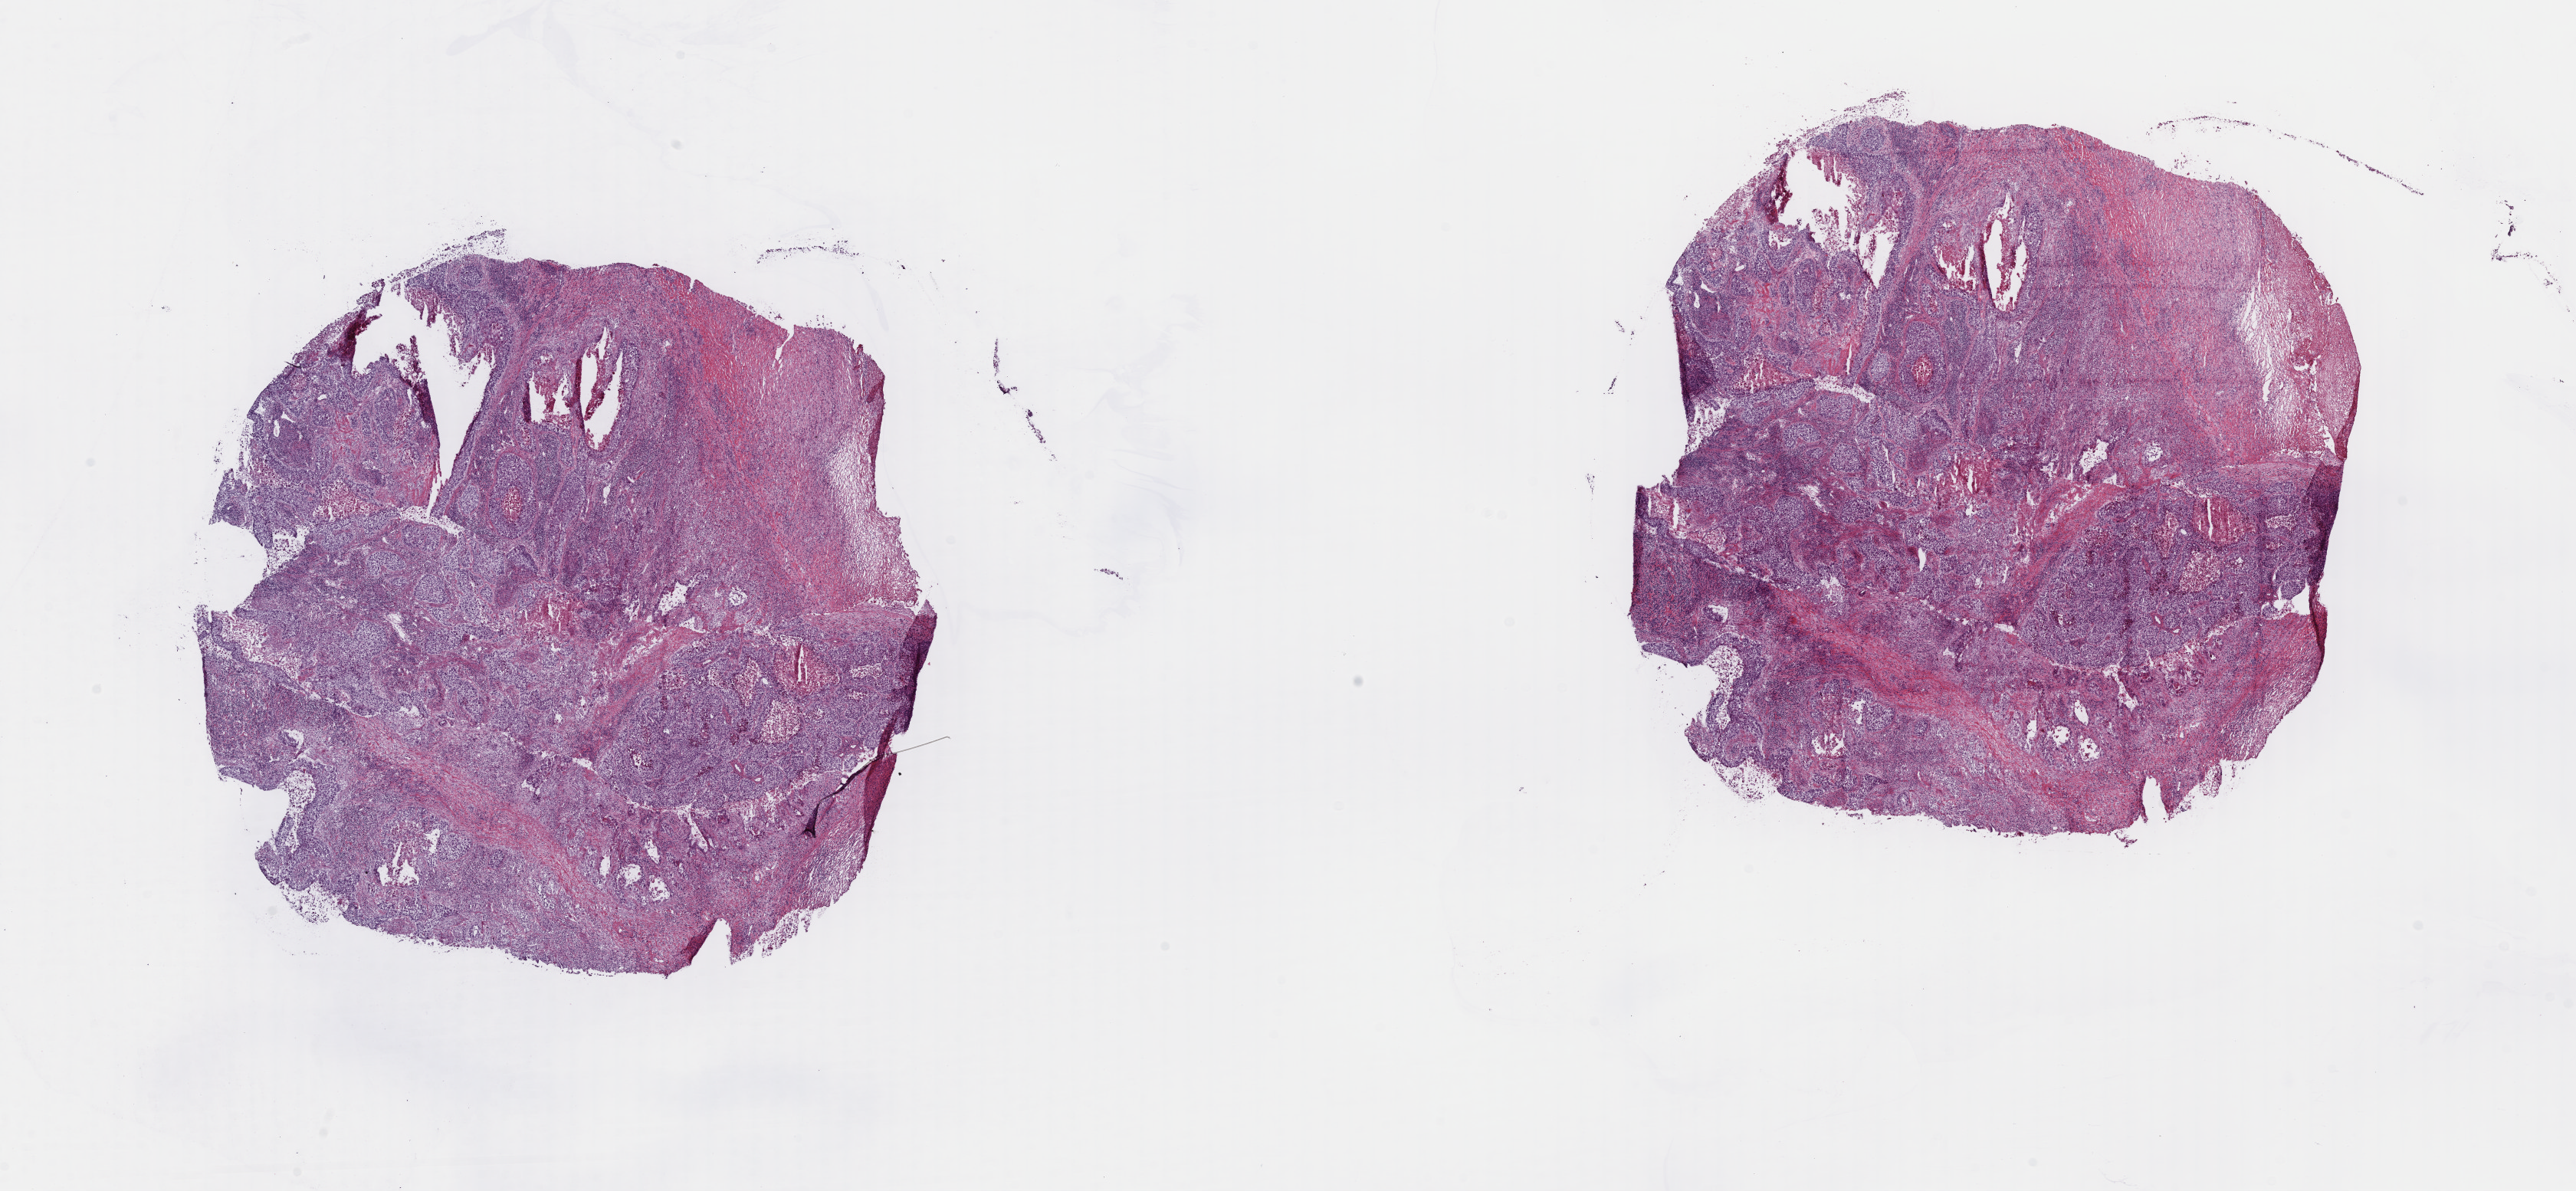
Whole-slide histology image, H&E-stained, a low-resolution overview of the entire scanned area, about 26.5 x 12.3 mm, frozen section from the top of the tissue portion, primary tumour sample from the lung. Patient: male, age at initial diagnosis 69 years. Slide review estimates, as recorded: tumour cells 60%, tumour nuclei 60%, normal cells 0%, stromal cells 35%, necrosis 5%. Inflammatory infiltration, as recorded: lymphocyte infiltration 10%, monocyte infiltration 2%, neutrophil infiltration 5%.
Pathologic diagnosis: Squamous cell carcinoma, NOS (lower lobe, lung). Laterality: right. AJCC pathologic stage: IIA. TNM: T2b N0 M0.